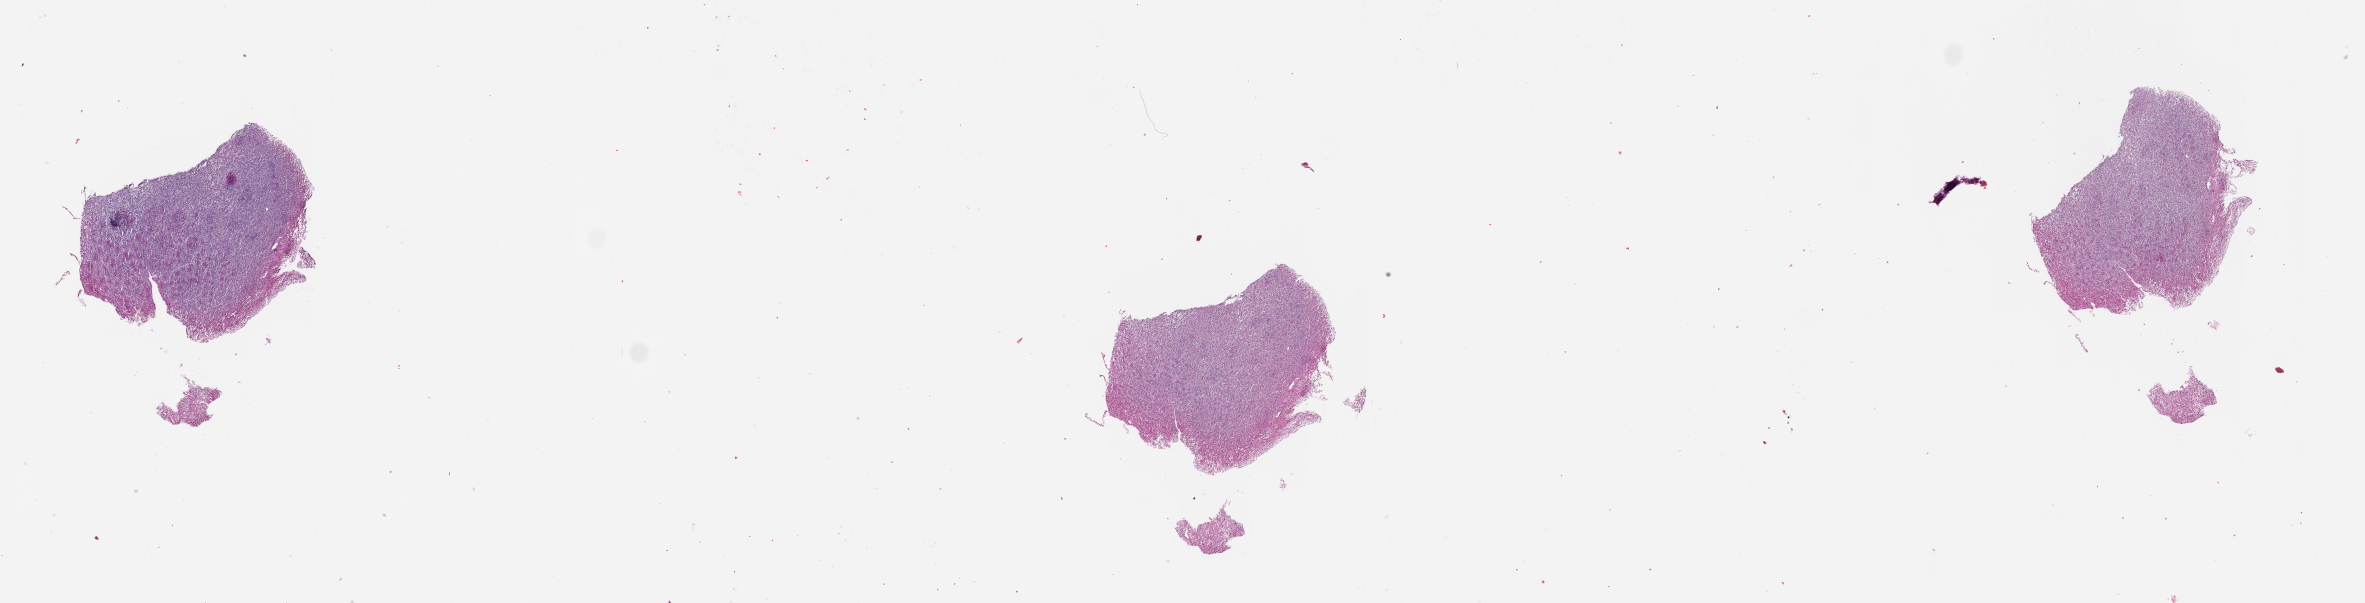
Digitized Hematoxylin and eosin (H&E) stained tissue section (whole slide) — shown as a low-resolution overview of the whole scanned area (about 38.1 x 9.7 mm, from a 20x scan). Brain, tumour tissue. 58-year-old male patient.
Primary tumour site (as recorded): frontal lobe. Histologic diagnosis: Glioblastoma.